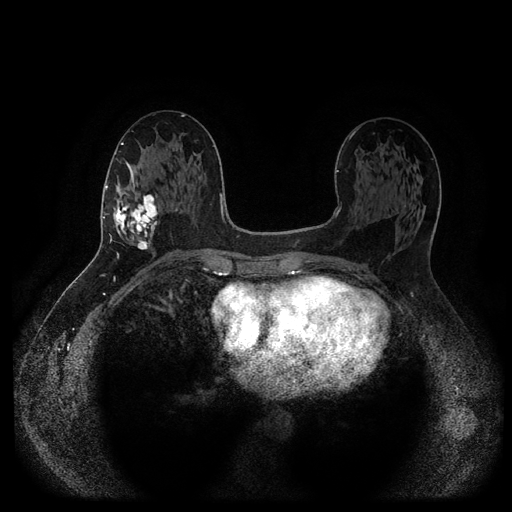
Breast MRI (dynamic contrast-enhanced, multi-phase), one axial slice. Position 49 of 116 along the scan axis. Dynamic contrast-enhanced series, time point 2 of 5 at this slice position (early post-contrast). 1.5 T. TE 2.6 ms, TR 5.3 ms. 2 mm slice thickness. 512 × 512 image matrix, field of view 360 × 360 mm. Patient: female, 58 years.
Outlined on this slice (semi-automatic segmentation, software-assisted and operator-edited):
- breast lesion (labelled 'tumour' in the annotation; benign lesions carry a separate 'benign' label): bounding box [x1, y1, x2, y2] px = [111, 194, 161, 251]